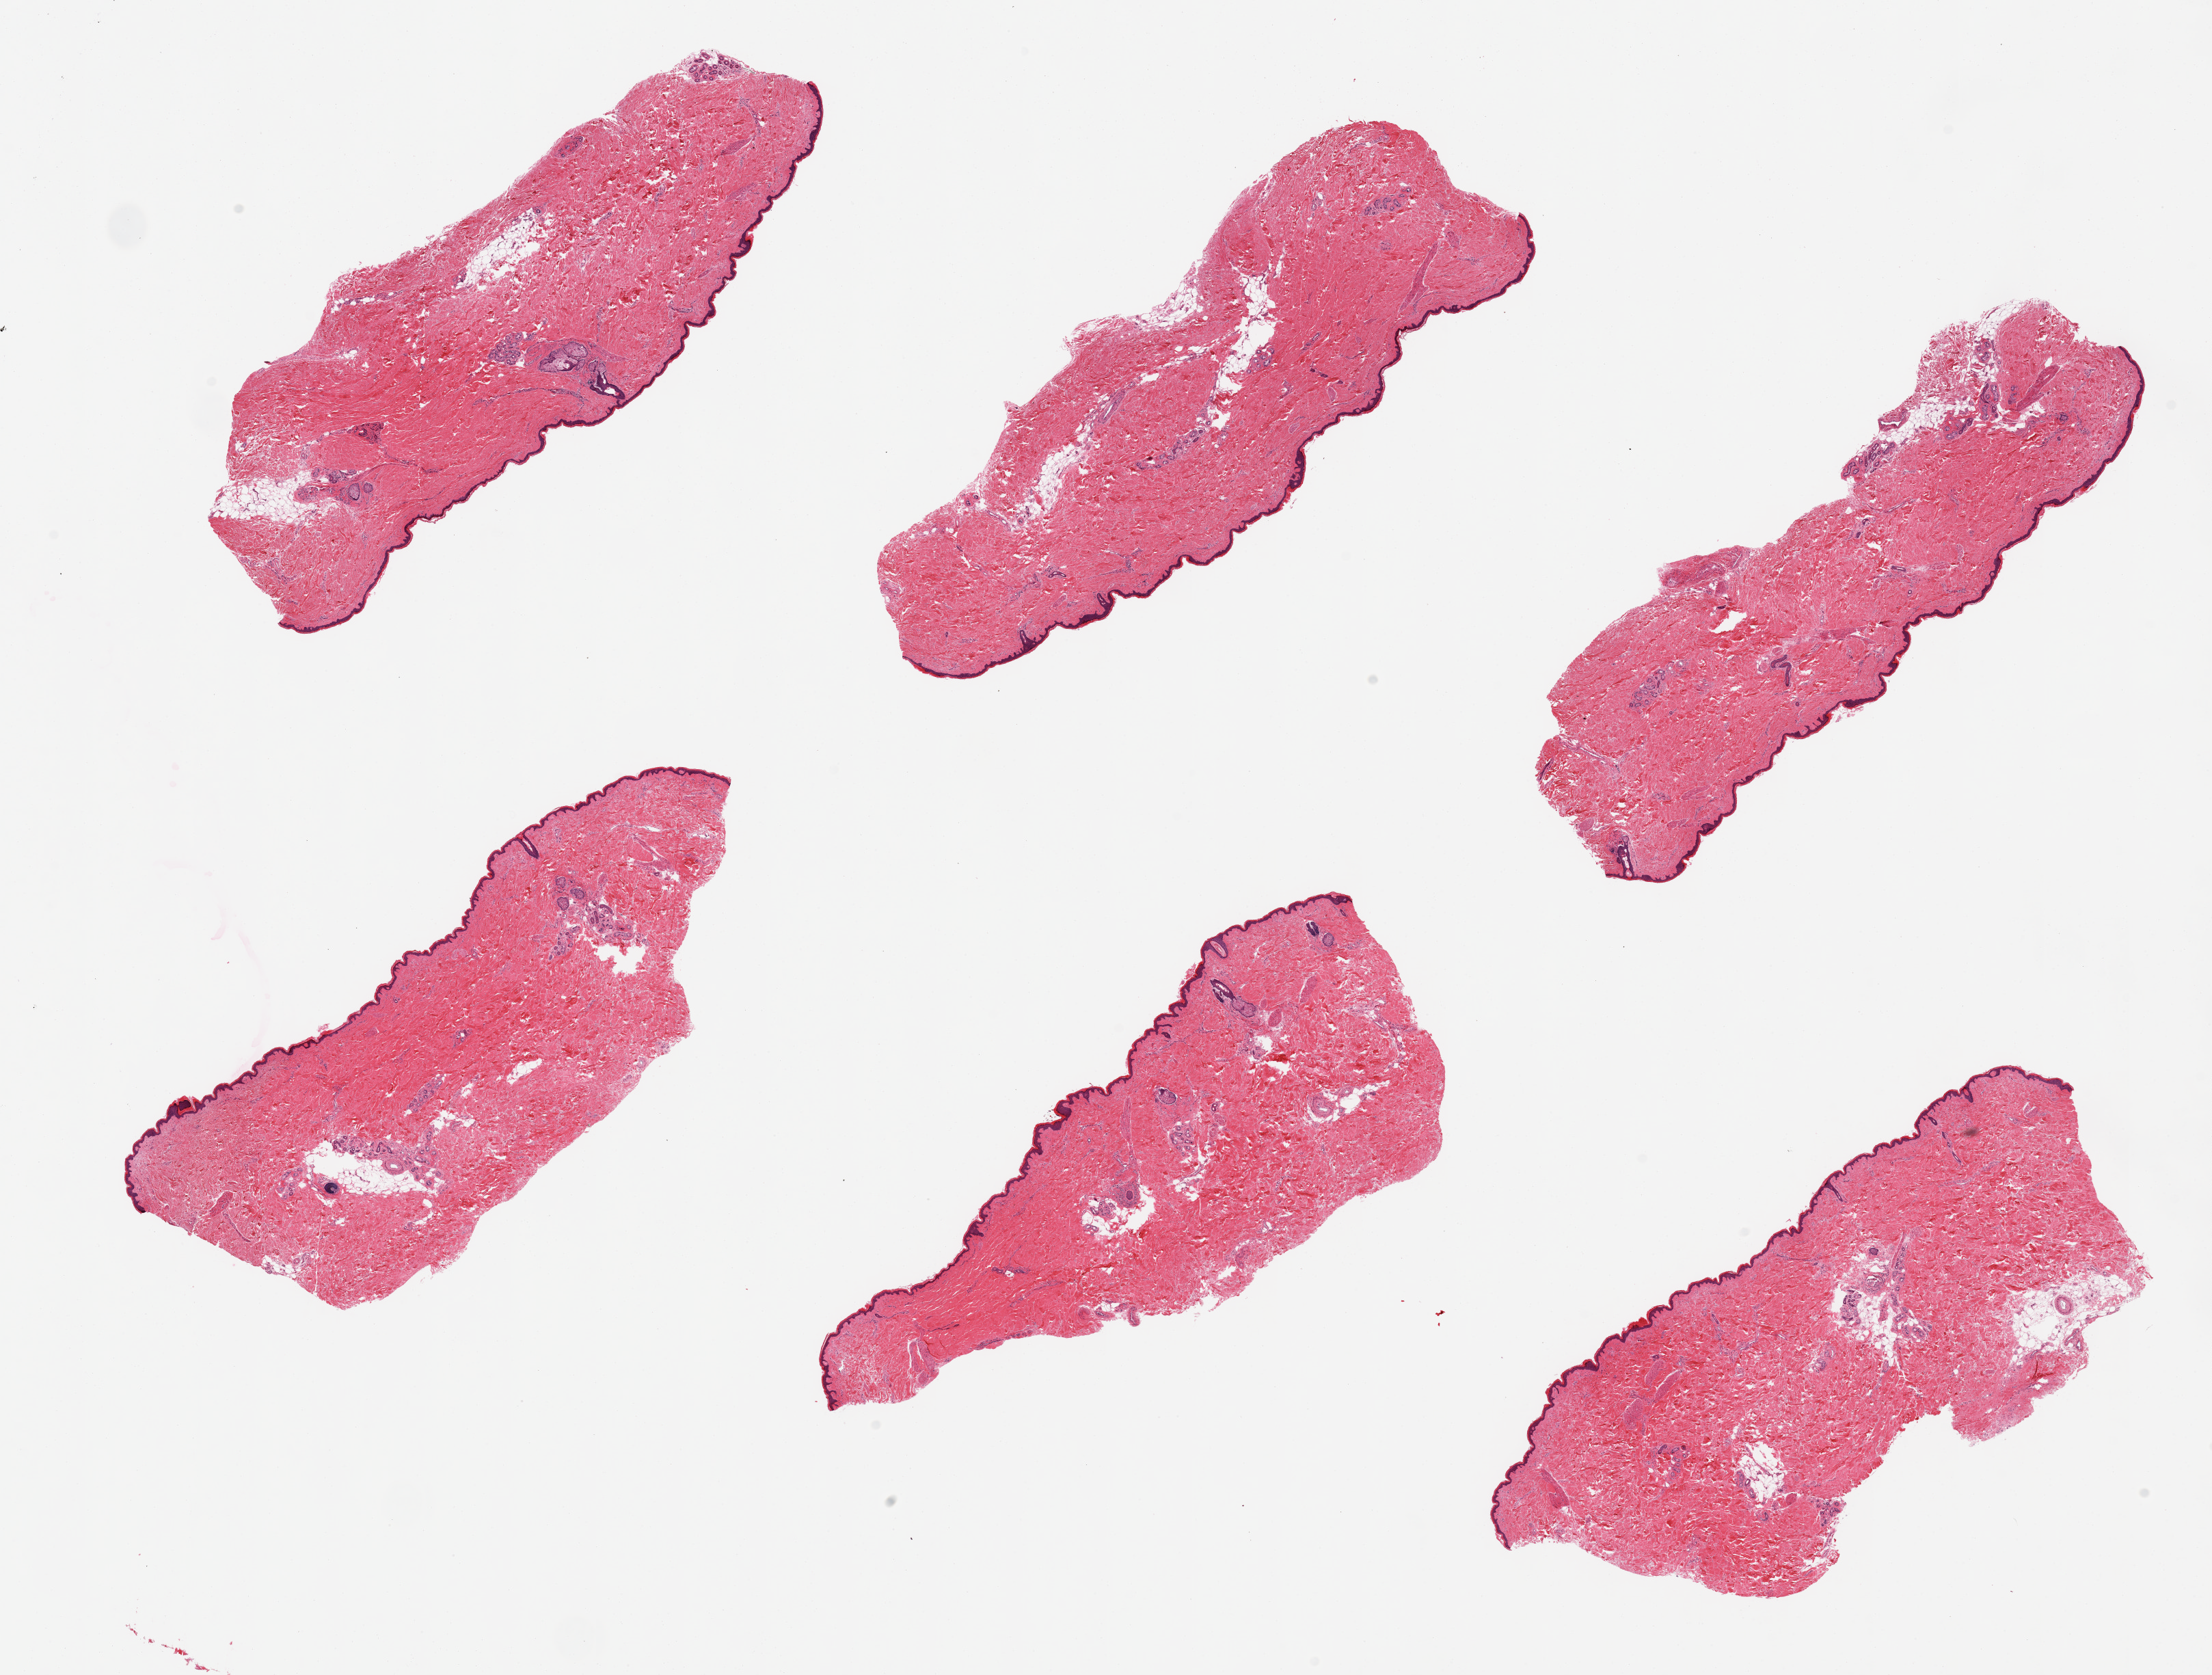
H&E whole-slide image, brightfield — a low-resolution overview of the entire scanned area, about 25.6 x 19.4 mm (acquisition: 20x scan), PAXgene-fixed paraffin-embedded (PFPE) section, sampled site (target tissue): skin of lower leg, donor tissue sample. Donor sex: male.
Pathologist's review note for this sample: 6 pieces; ~10% internal/periadnexal fat, 31um thick epidermis.